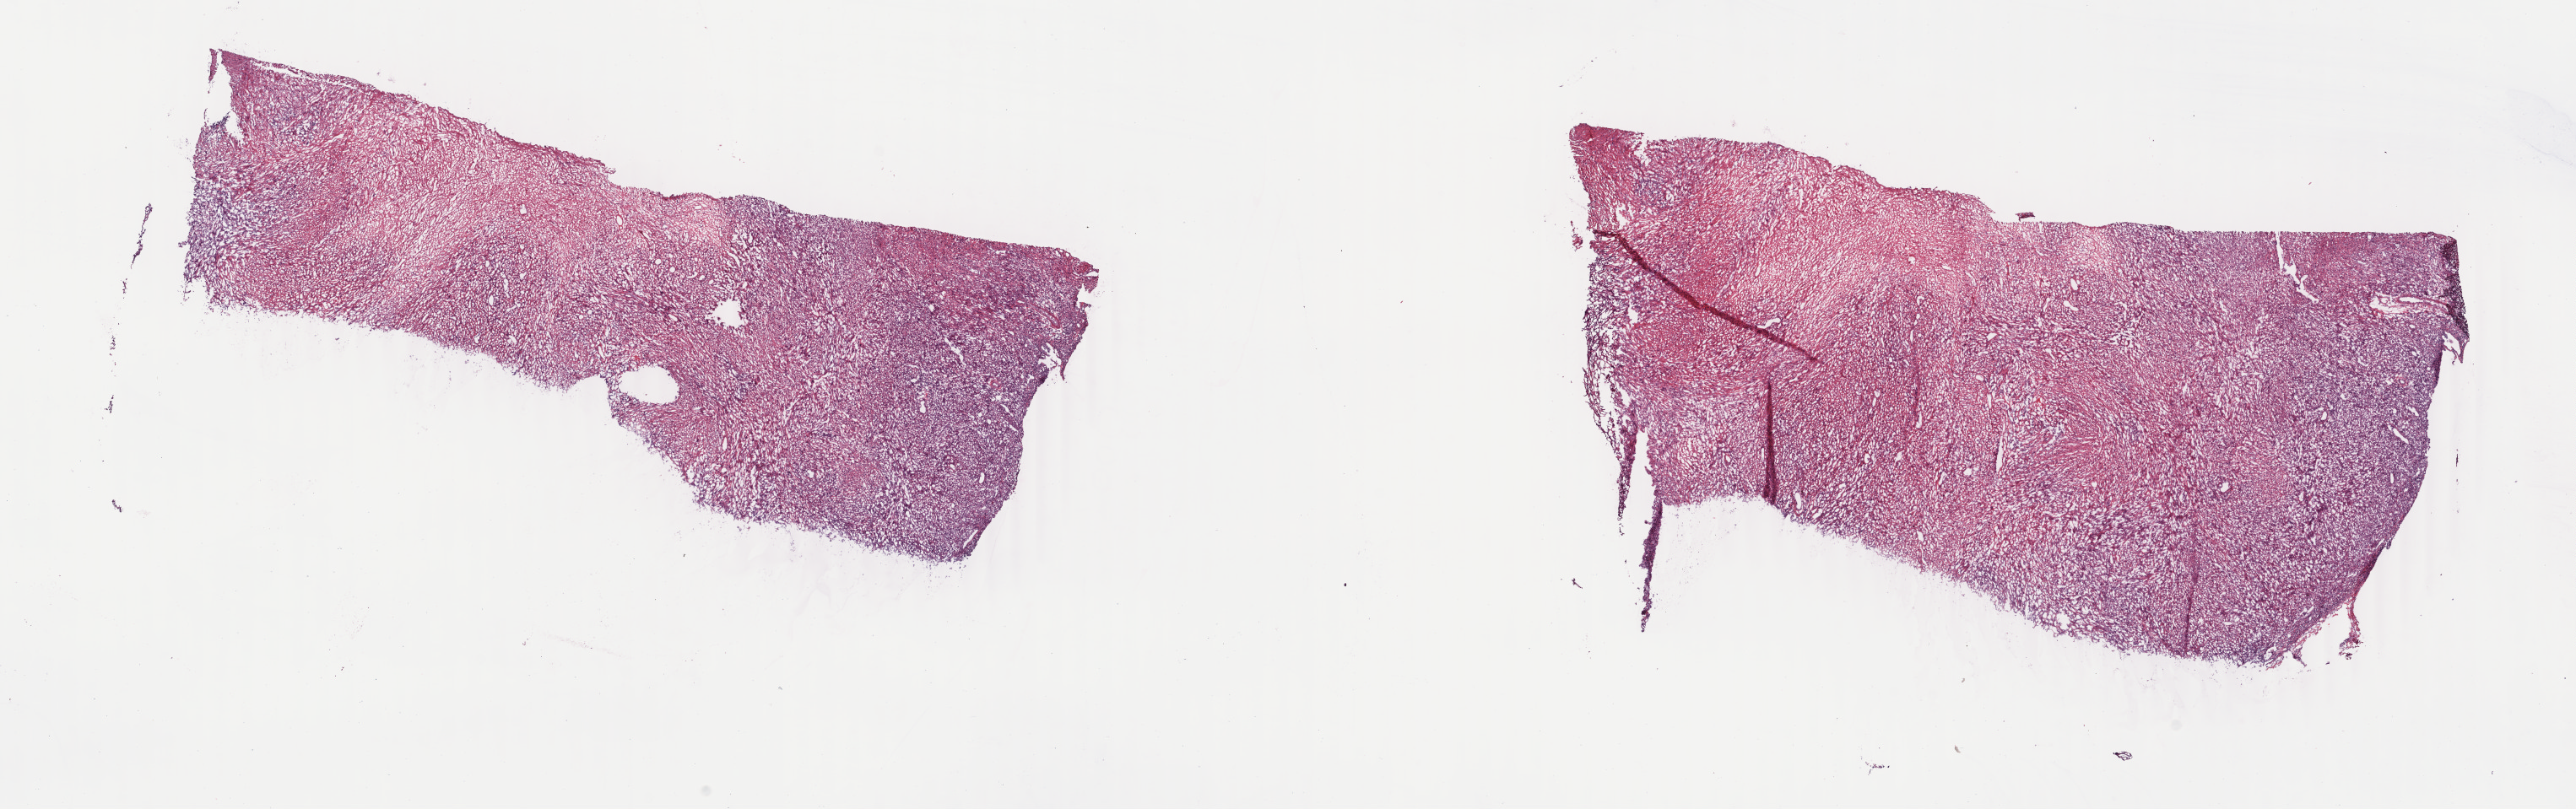
Whole-slide histology image, H&E-stained — a low-resolution overview of the entire scanned area, about 24.3 x 7.6 mm, frozen section, mesothelium, primary tumour sample. Male patient; age at initial diagnosis 67 years. Composition of this section per pathologist review: tumour cells 100%, tumour nuclei 80%, normal cells 0%, stromal cells 0%, necrosis 0%. Infiltration values recorded for this section: lymphocyte infiltration 2%, monocyte infiltration 0%, neutrophil infiltration 0%.
TNM: T3 N0 M0. AJCC pathologic stage: III (5th edition). Laterality: right. Diagnosis: Mesothelioma, biphasic, malignant (pleura, NOS).